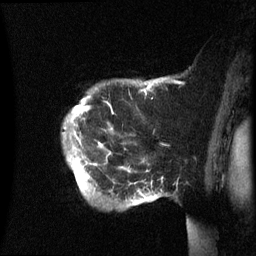
Breast MRI (dynamic contrast-enhanced), one sagittal slice; dynamic contrast-enhanced series, image 2 of 3 at this slice position (ordered by acquisition); 1.5 T; TE 4.2 ms, TR 8.4 ms; 256 × 256 image matrix, field of view 230 × 230 mm. Patient: female, 49 years.
Annotated regions visible in this slice (semi-automatic segmentation, software-assisted and operator-edited):
- analysis volume of interest (the breast-tissue region the enhancement analysis was run in; not a lesion): bounding box <63,77,169,209> (left, top, right, bottom; pixels)
- tumour enhancement mask (voxels above the 70 % enhancement threshold inside the analysis volume of interest): <83,86,150,111>